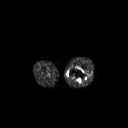
FDG PET of an extremity soft-tissue mass (from a PET/CT study), one axial slice; slice 222 of 267 in the series (ordered by position); 128 × 128 image matrix, field of view 700 × 700 mm. Patient: male, 44 years. Case-level facts recorded for this patient, not image findings: histological type: undifferentiated pleomorphic liposarcoma; grade: high; site of the primary tumour: left thigh.
Structures marked on this image (expert contour drawn on MRI and transferred to this co-registered scan by the dataset authors):
- gross tumour volume including surrounding oedema: box from (x=68, y=67) to (x=87, y=83) px
- gross tumour volume (mass): (x=68, y=67)–(x=87, y=83)